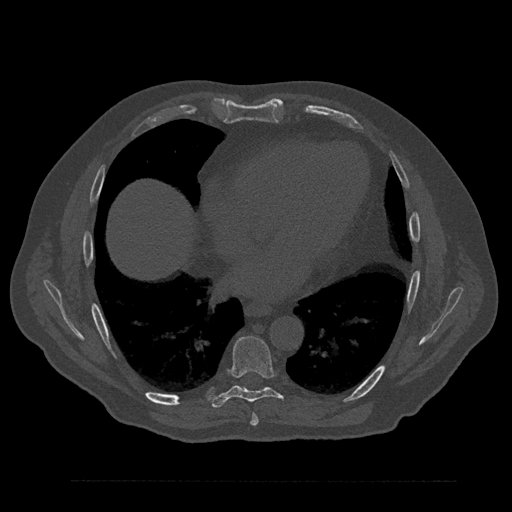
CT including the spine, one axial slice; position 454 of 797 along the scan axis; reconstruction kernel Br40s/3; 120 kVp; bone window (W 1800 / L 400 HU); 512 × 512 image matrix. Patient: male, 61 years. From the clinical record (not read from this slice): primary cancer: prostate.
Structures marked on this image (semi-automatic segmentation, software-assisted and operator-edited):
- T7 vertebra: bounding box (x1, y1, x2, y2) in pixels: (250, 414, 259, 426)
- T8 vertebra: (210, 335, 283, 408)